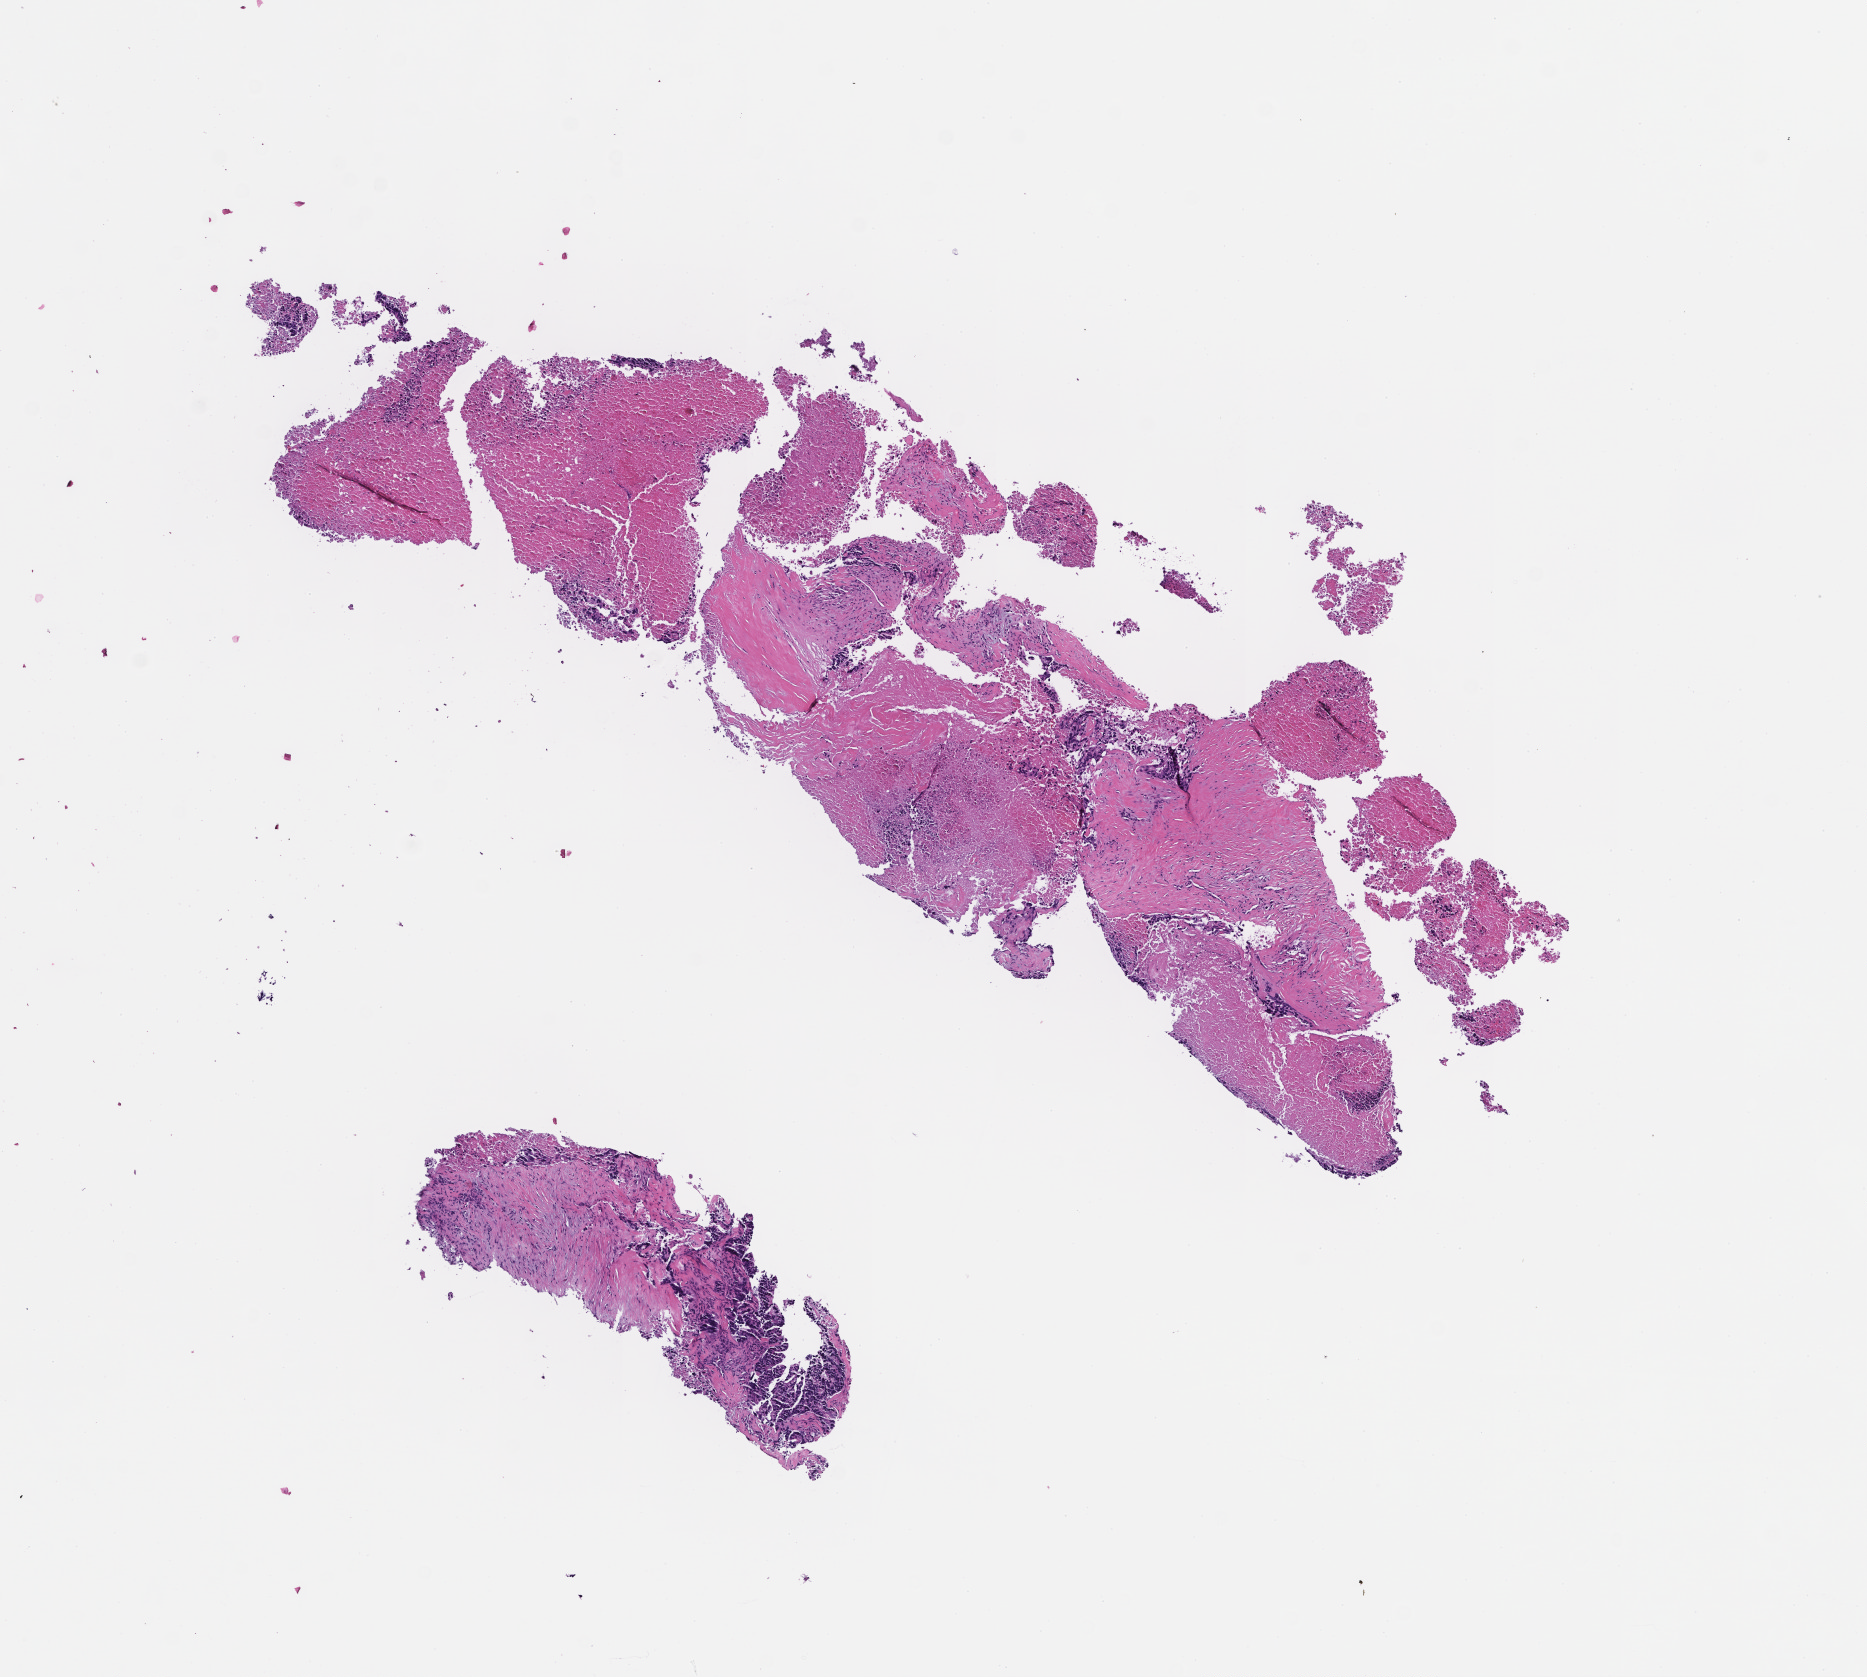
Whole-slide image, haematoxylin and eosin stain, whole scanned area (about 7.5 x 6.8 mm) shown as a low-resolution overview. FFPE section. Archival tissue. Female patient.
This section: metastatic tumor tissue. Patient diagnosis (primary): Colorectal Carcinoma.